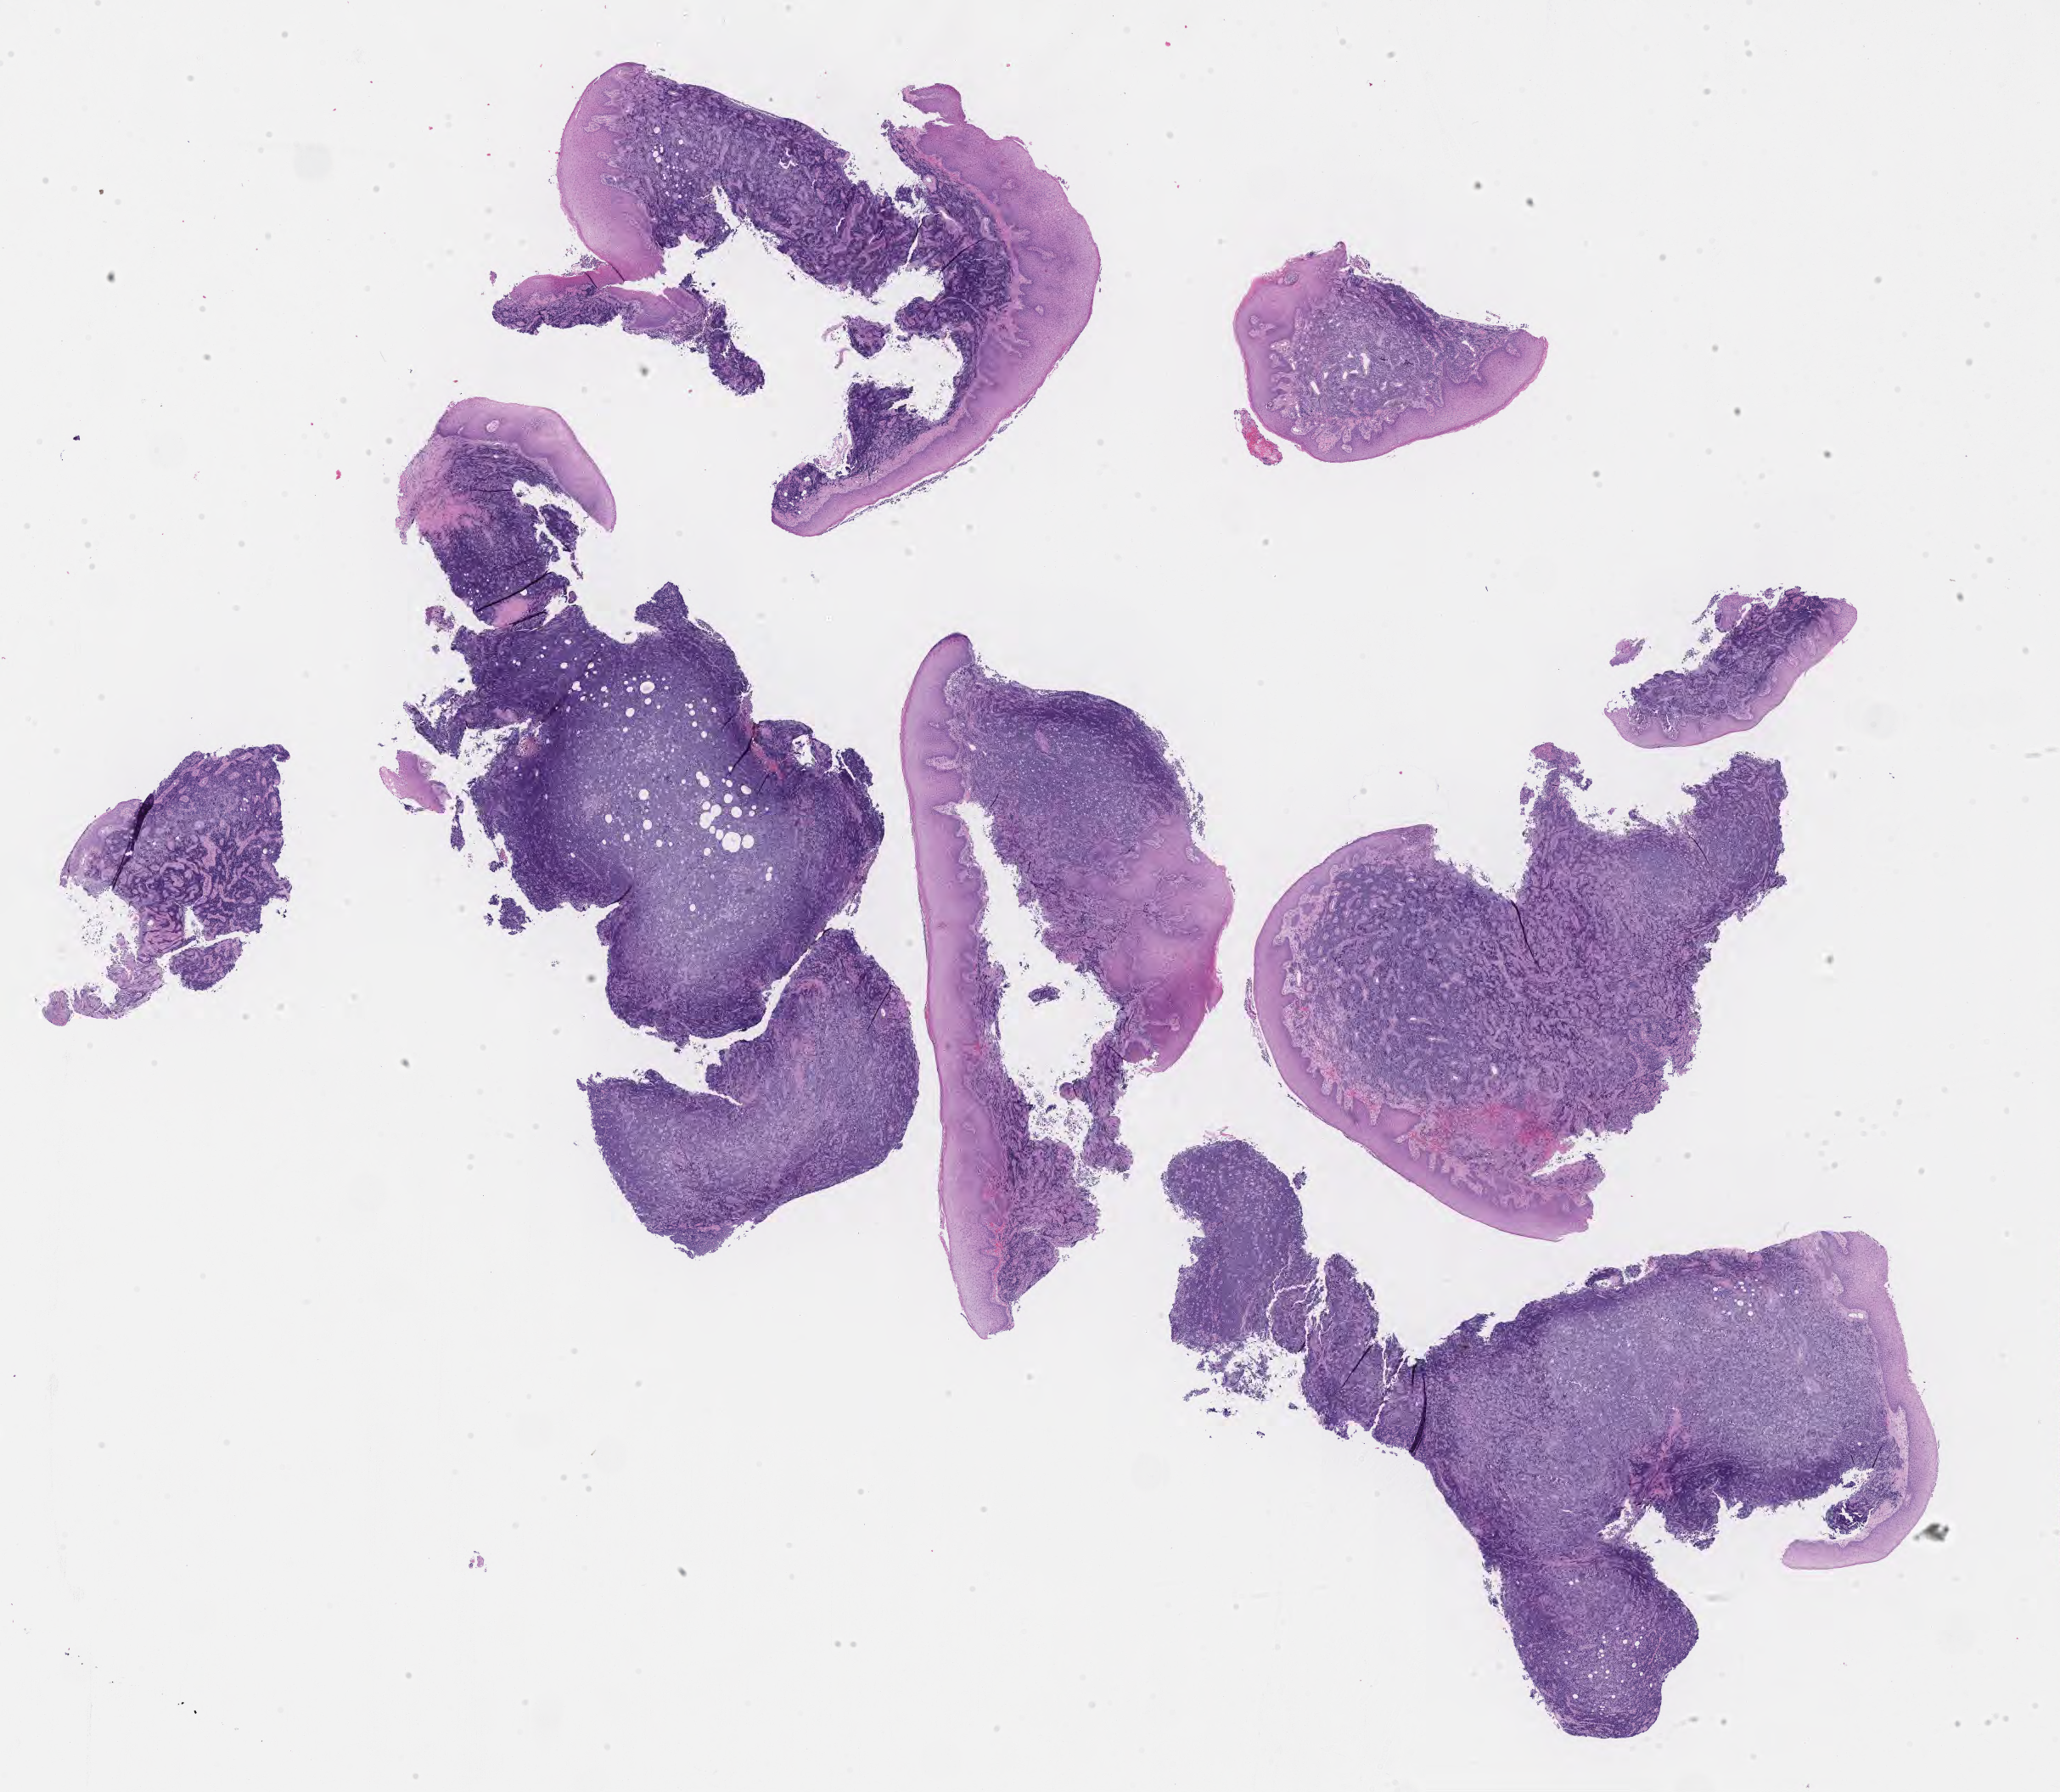
H&E whole-slide image — shown as a low-resolution overview of the whole scanned area (about 19.6 x 17.1 mm); specimen: tumor tissue. Patient: male, age 43 years.
Diagnosis: Burkitt lymphoma, NOS.